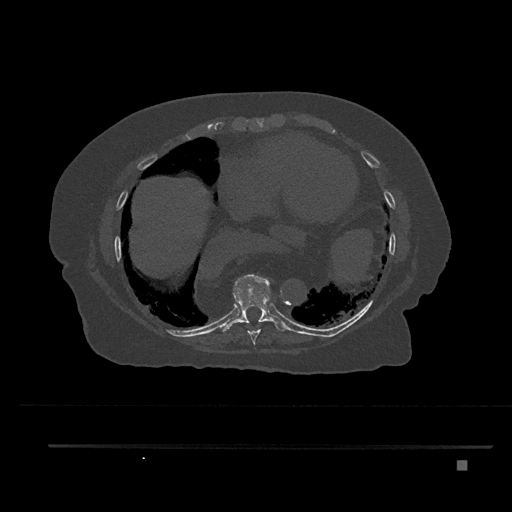
CT including the spine, one axial slice; position 417 of 797 along the scan axis; bone window (W 1800 / L 400 HU); 0.5 mm slice thickness; 512 × 512 image matrix, field of view 437 × 437 mm. Female patient, age 76 years. From the clinical record (not read from this slice): primary cancer: lung; vertebrae with lytic lesions (as recorded): T11, L3.
Outlined on this slice (semi-automatic segmentation, software-assisted and operator-edited):
- T8 vertebra: bounding box [x1, y1, x2, y2] px = [247, 328, 261, 346]
- T9 vertebra: [220, 274, 288, 332]